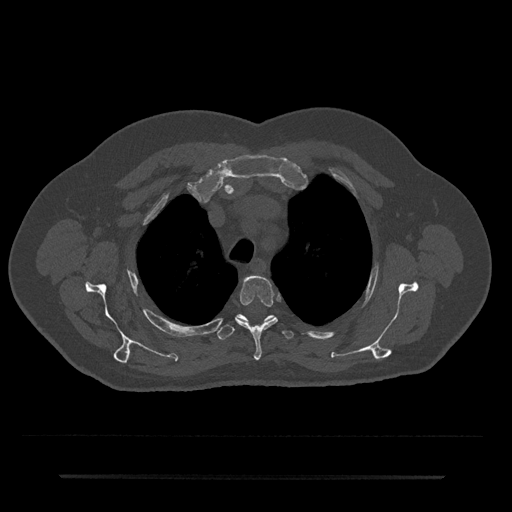
CT including the spine, one axial slice; position 557 of 797 along the scan axis; reconstruction kernel Br40s/3; 120 kVp; bone window (W 1800 / L 400 HU); 0.5 mm slice thickness; 512 × 512 image matrix. Male patient, age 69 years. From the clinical record (not read from this slice): primary cancer: prostate.
Outlined on this slice (semi-automatic segmentation, software-assisted and operator-edited):
- T3 vertebra: bounding box (x1, y1, x2, y2) in pixels: (236, 275, 278, 360)
- T4 vertebra: (217, 314, 294, 340)